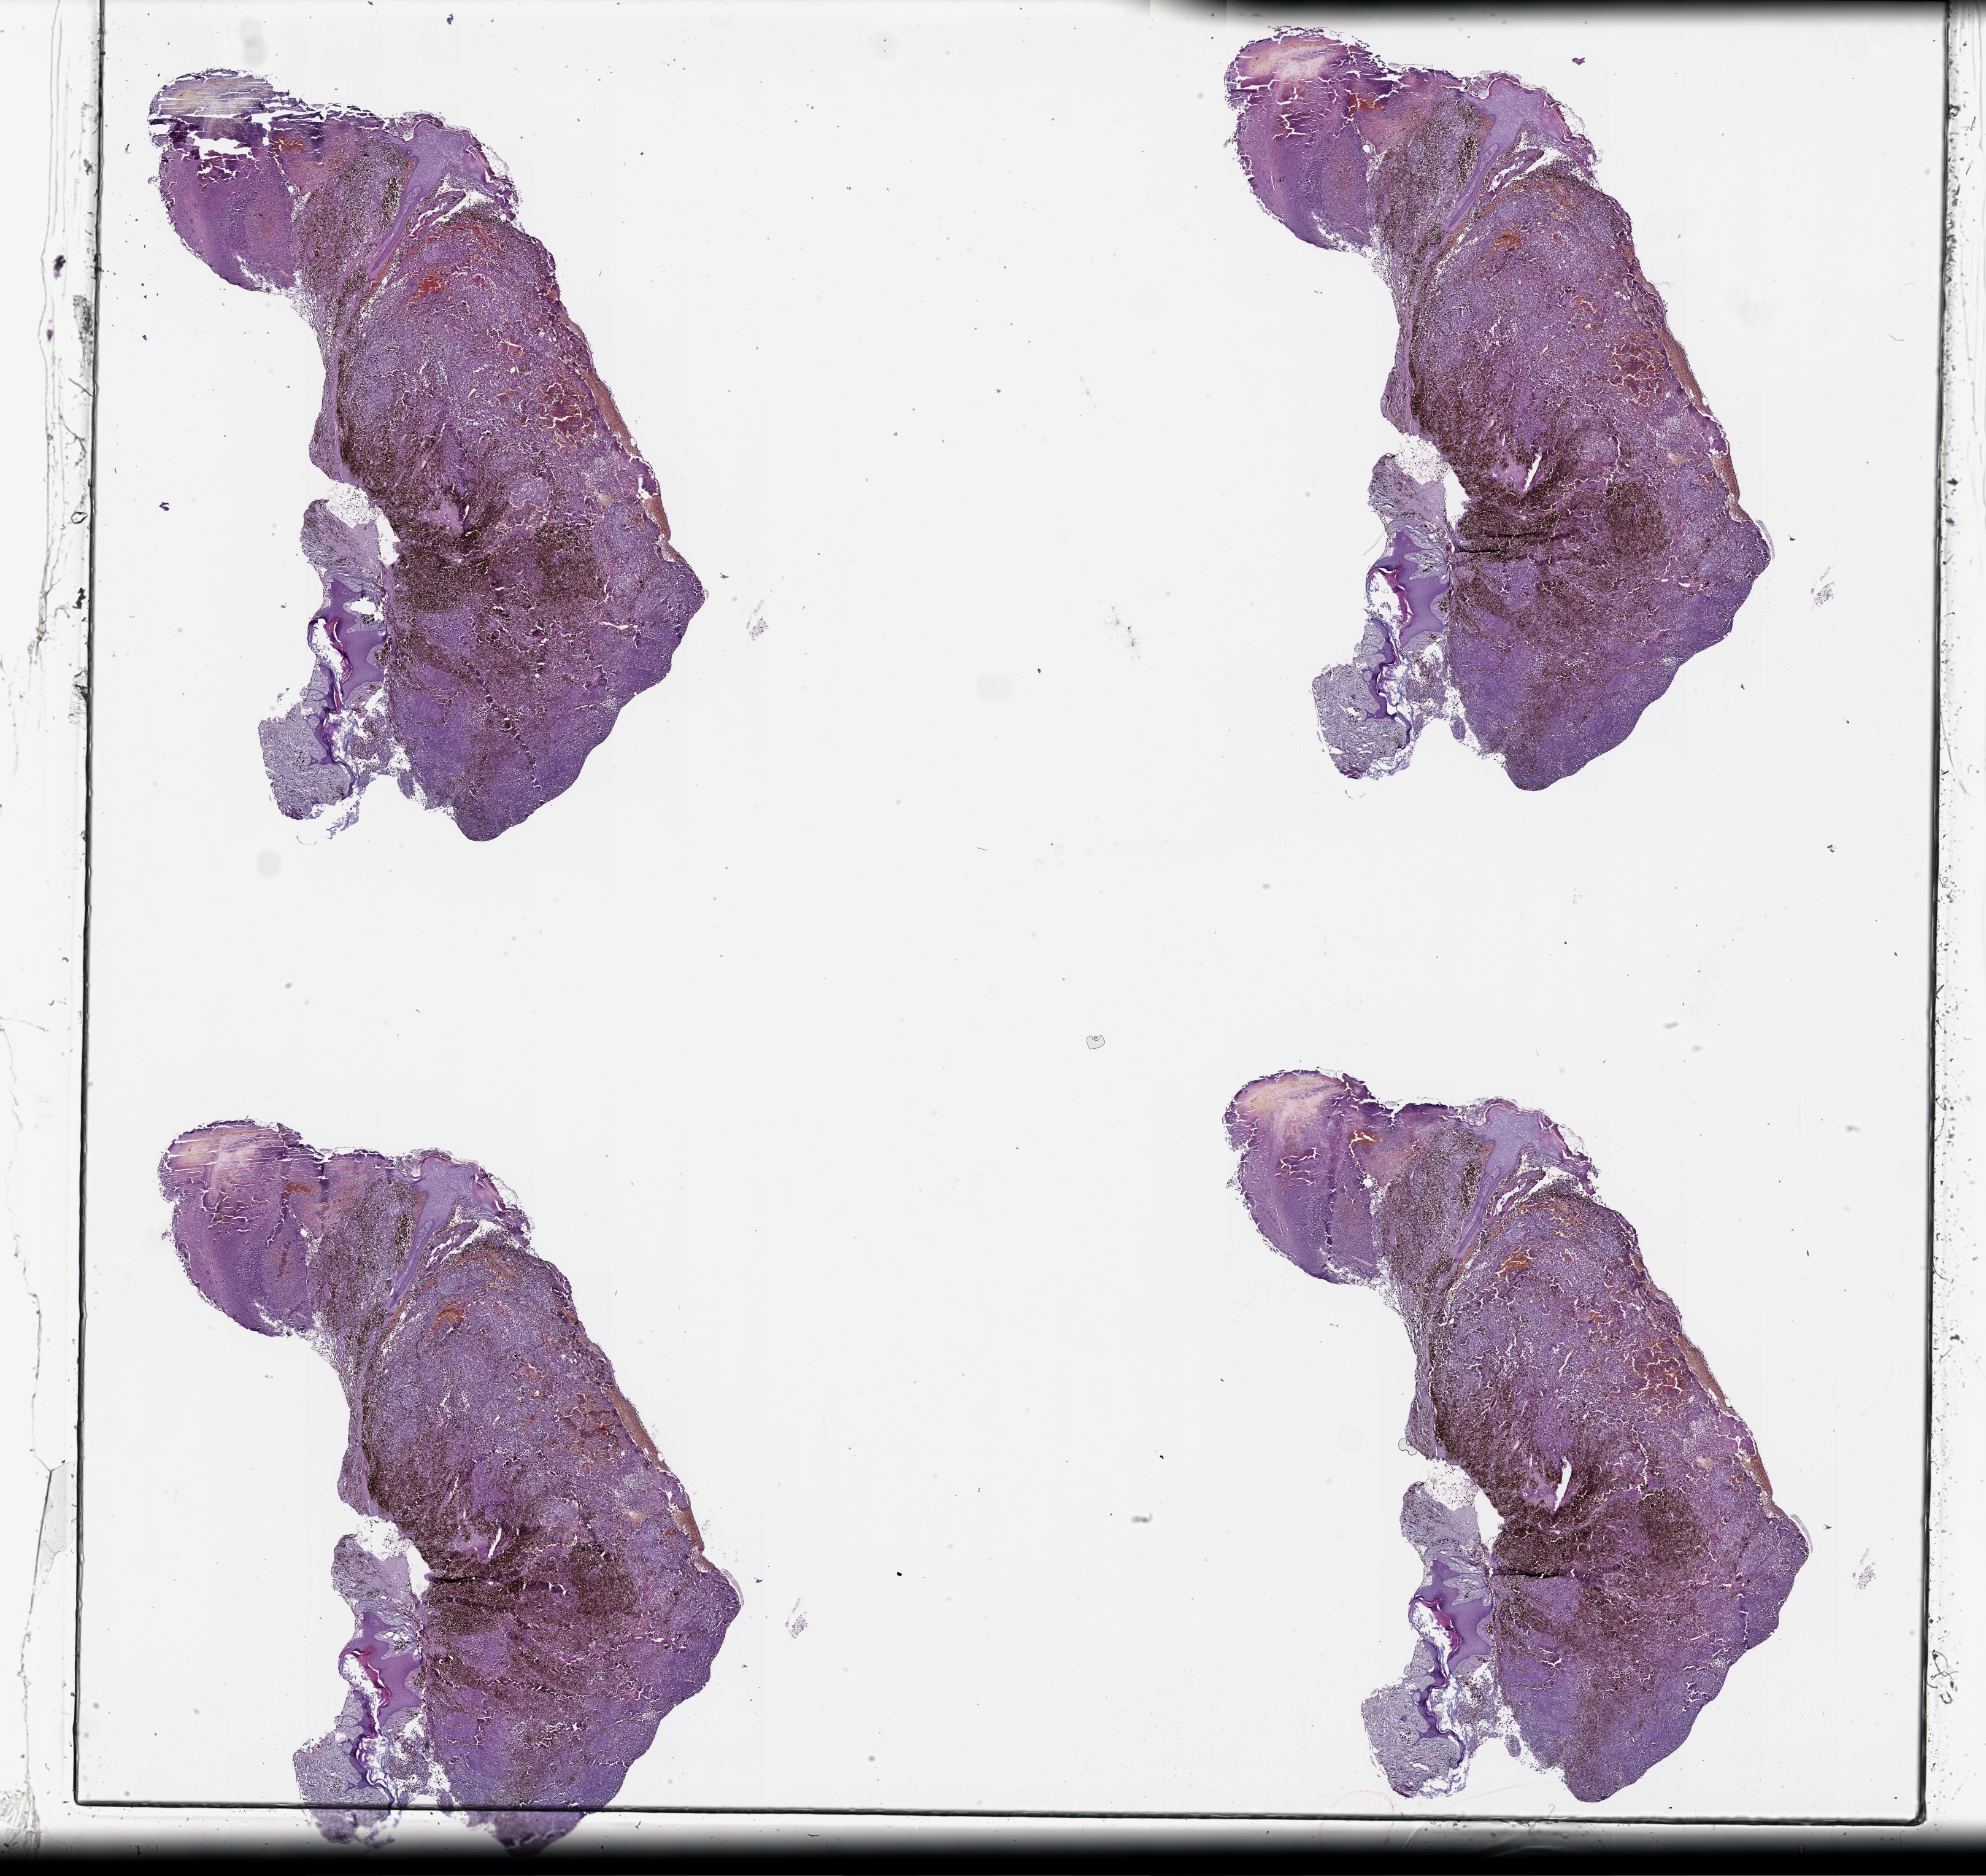
Digitized H&E tissue section (whole slide), a low-resolution overview of the entire scanned area, about 26.1 x 24.6 mm; melanoma tumour tissue; sampled site not recorded. Patient: female, age 81 years.
Histologic diagnosis: Malignant melanoma, NOS.